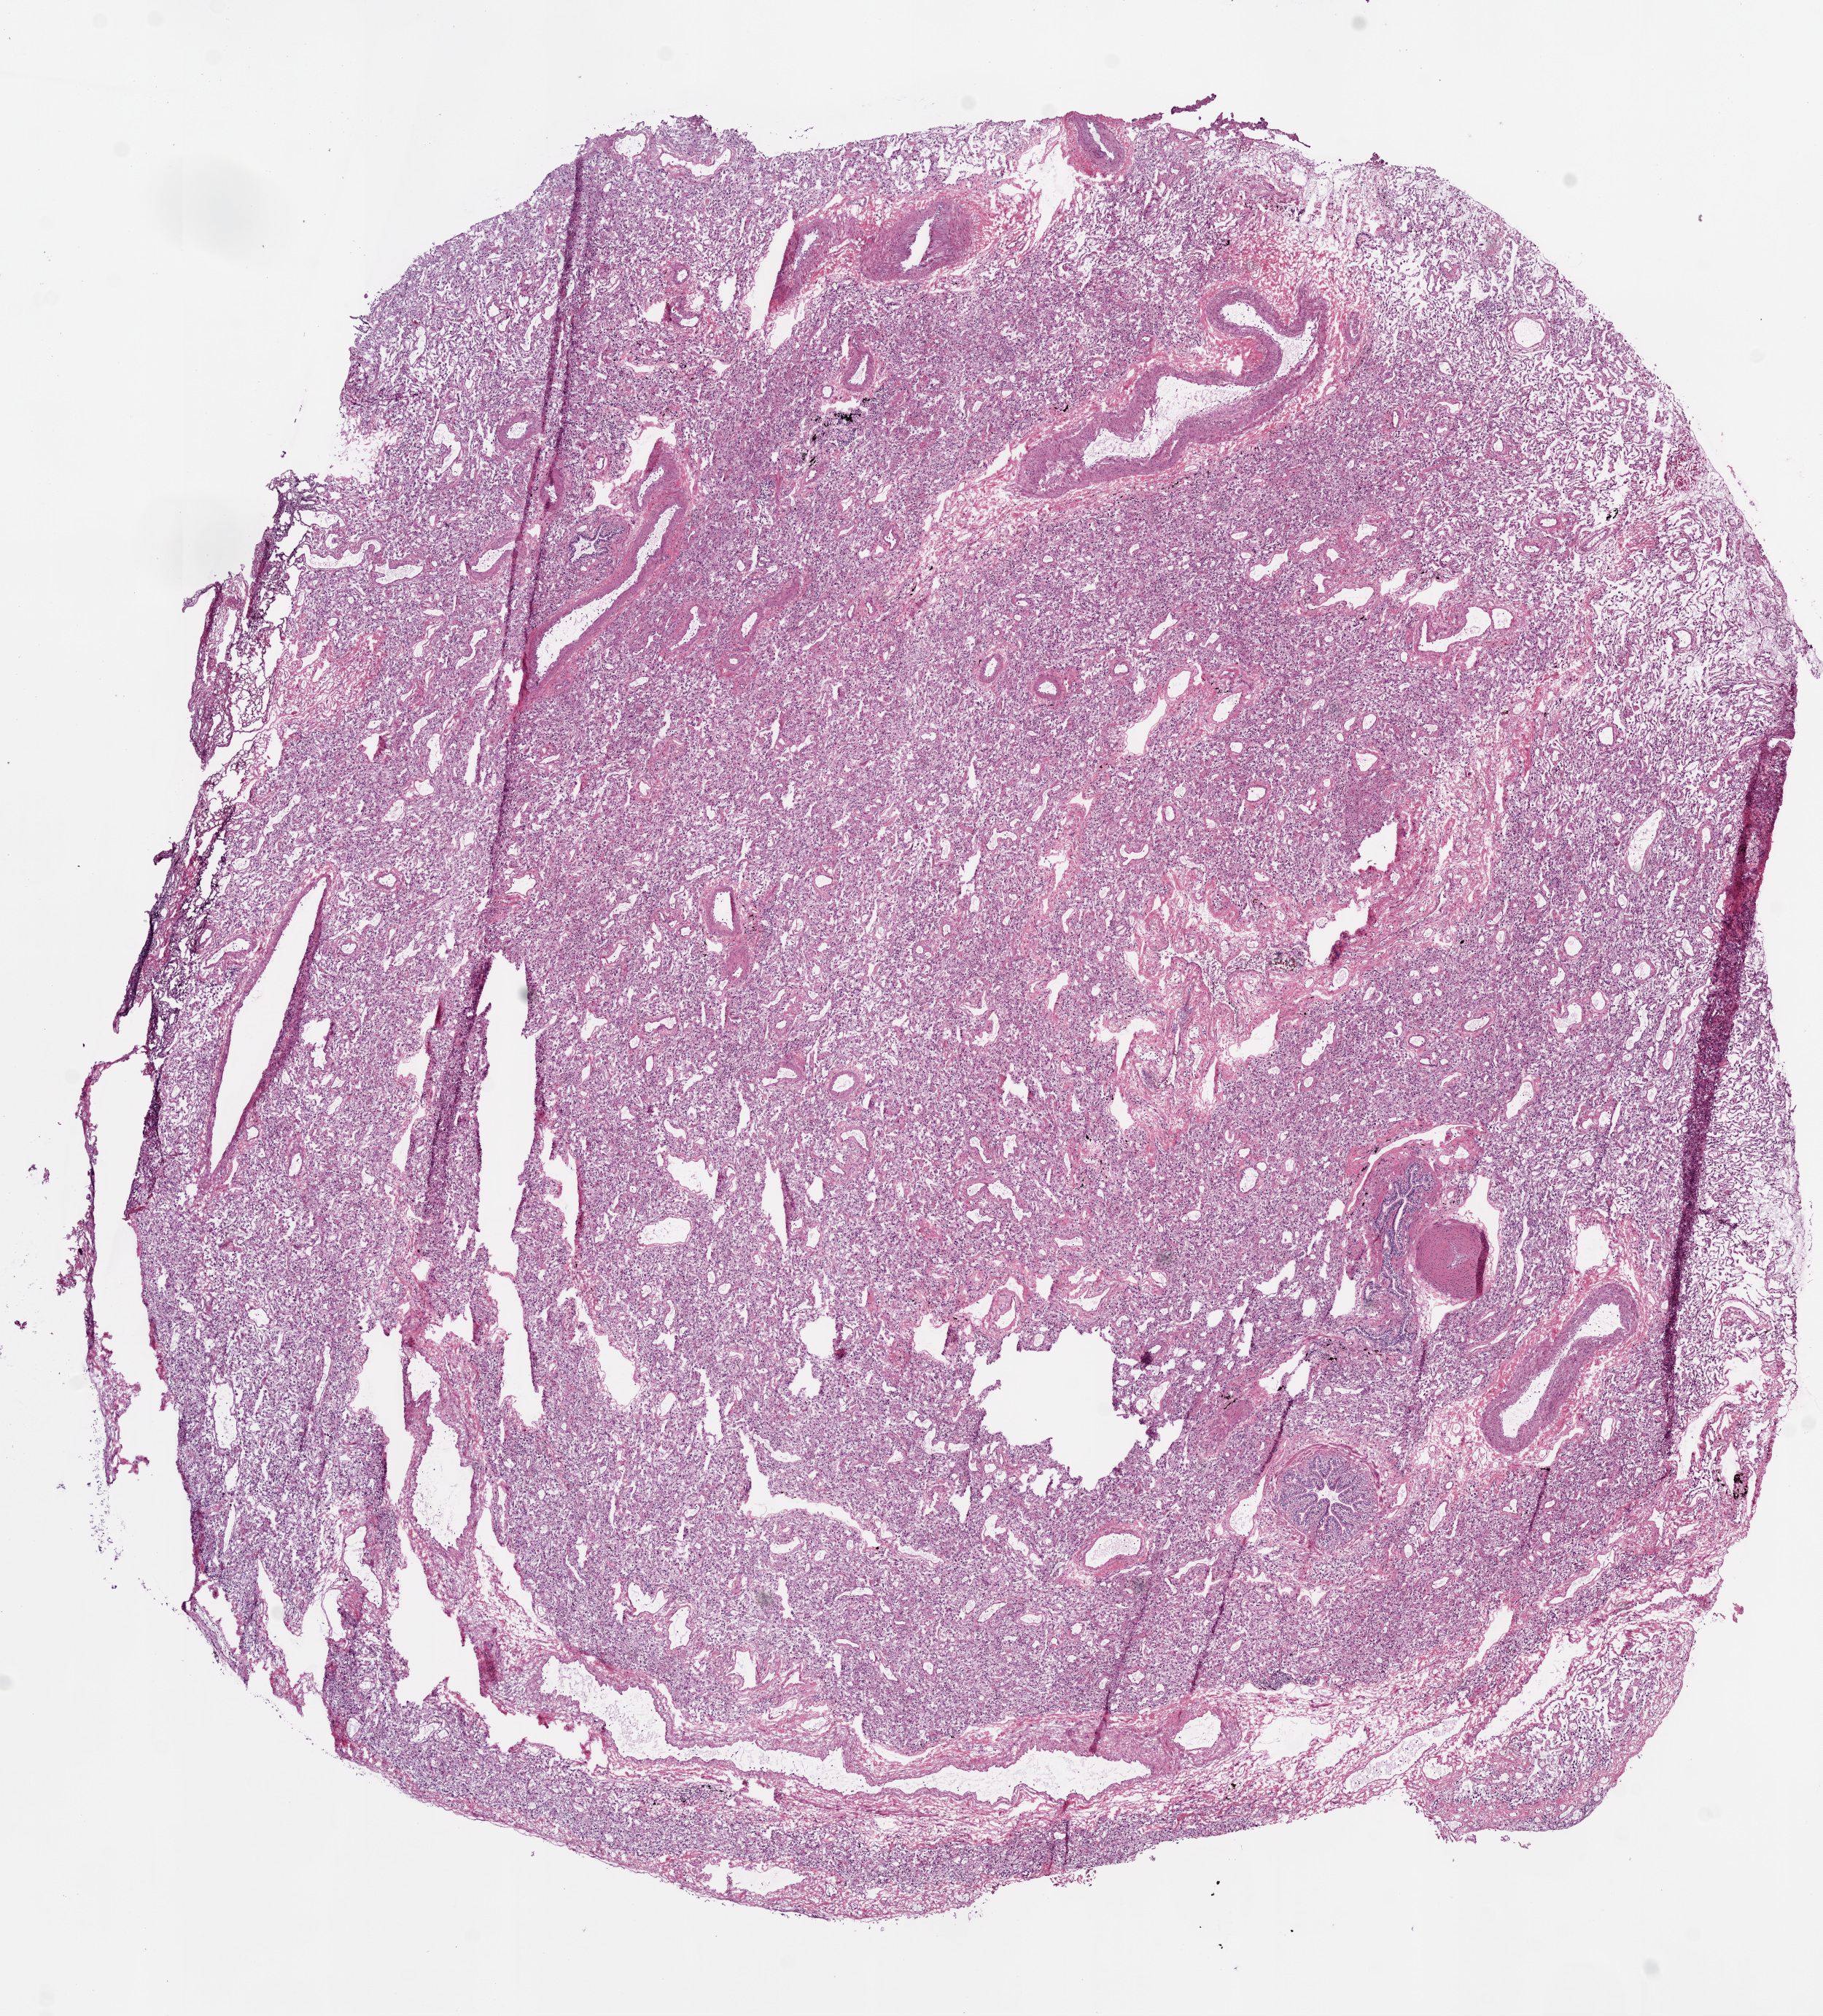
Whole-slide histology image, Hematoxylin and eosin (H&E) stained — low-resolution overview of the scanned area, about 10.0 x 11.1 mm (acquisition: 20x scan). Frozen section from the bottom of the tissue portion. Solid tissue normal (non-tumour tissue) sample from the lung. Patient: male, age at initial diagnosis 73 years.
This section: solid tissue normal (non-tumour) sample from the same patient. Patient diagnosis: Squamous cell carcinoma, NOS (lower lobe, lung).